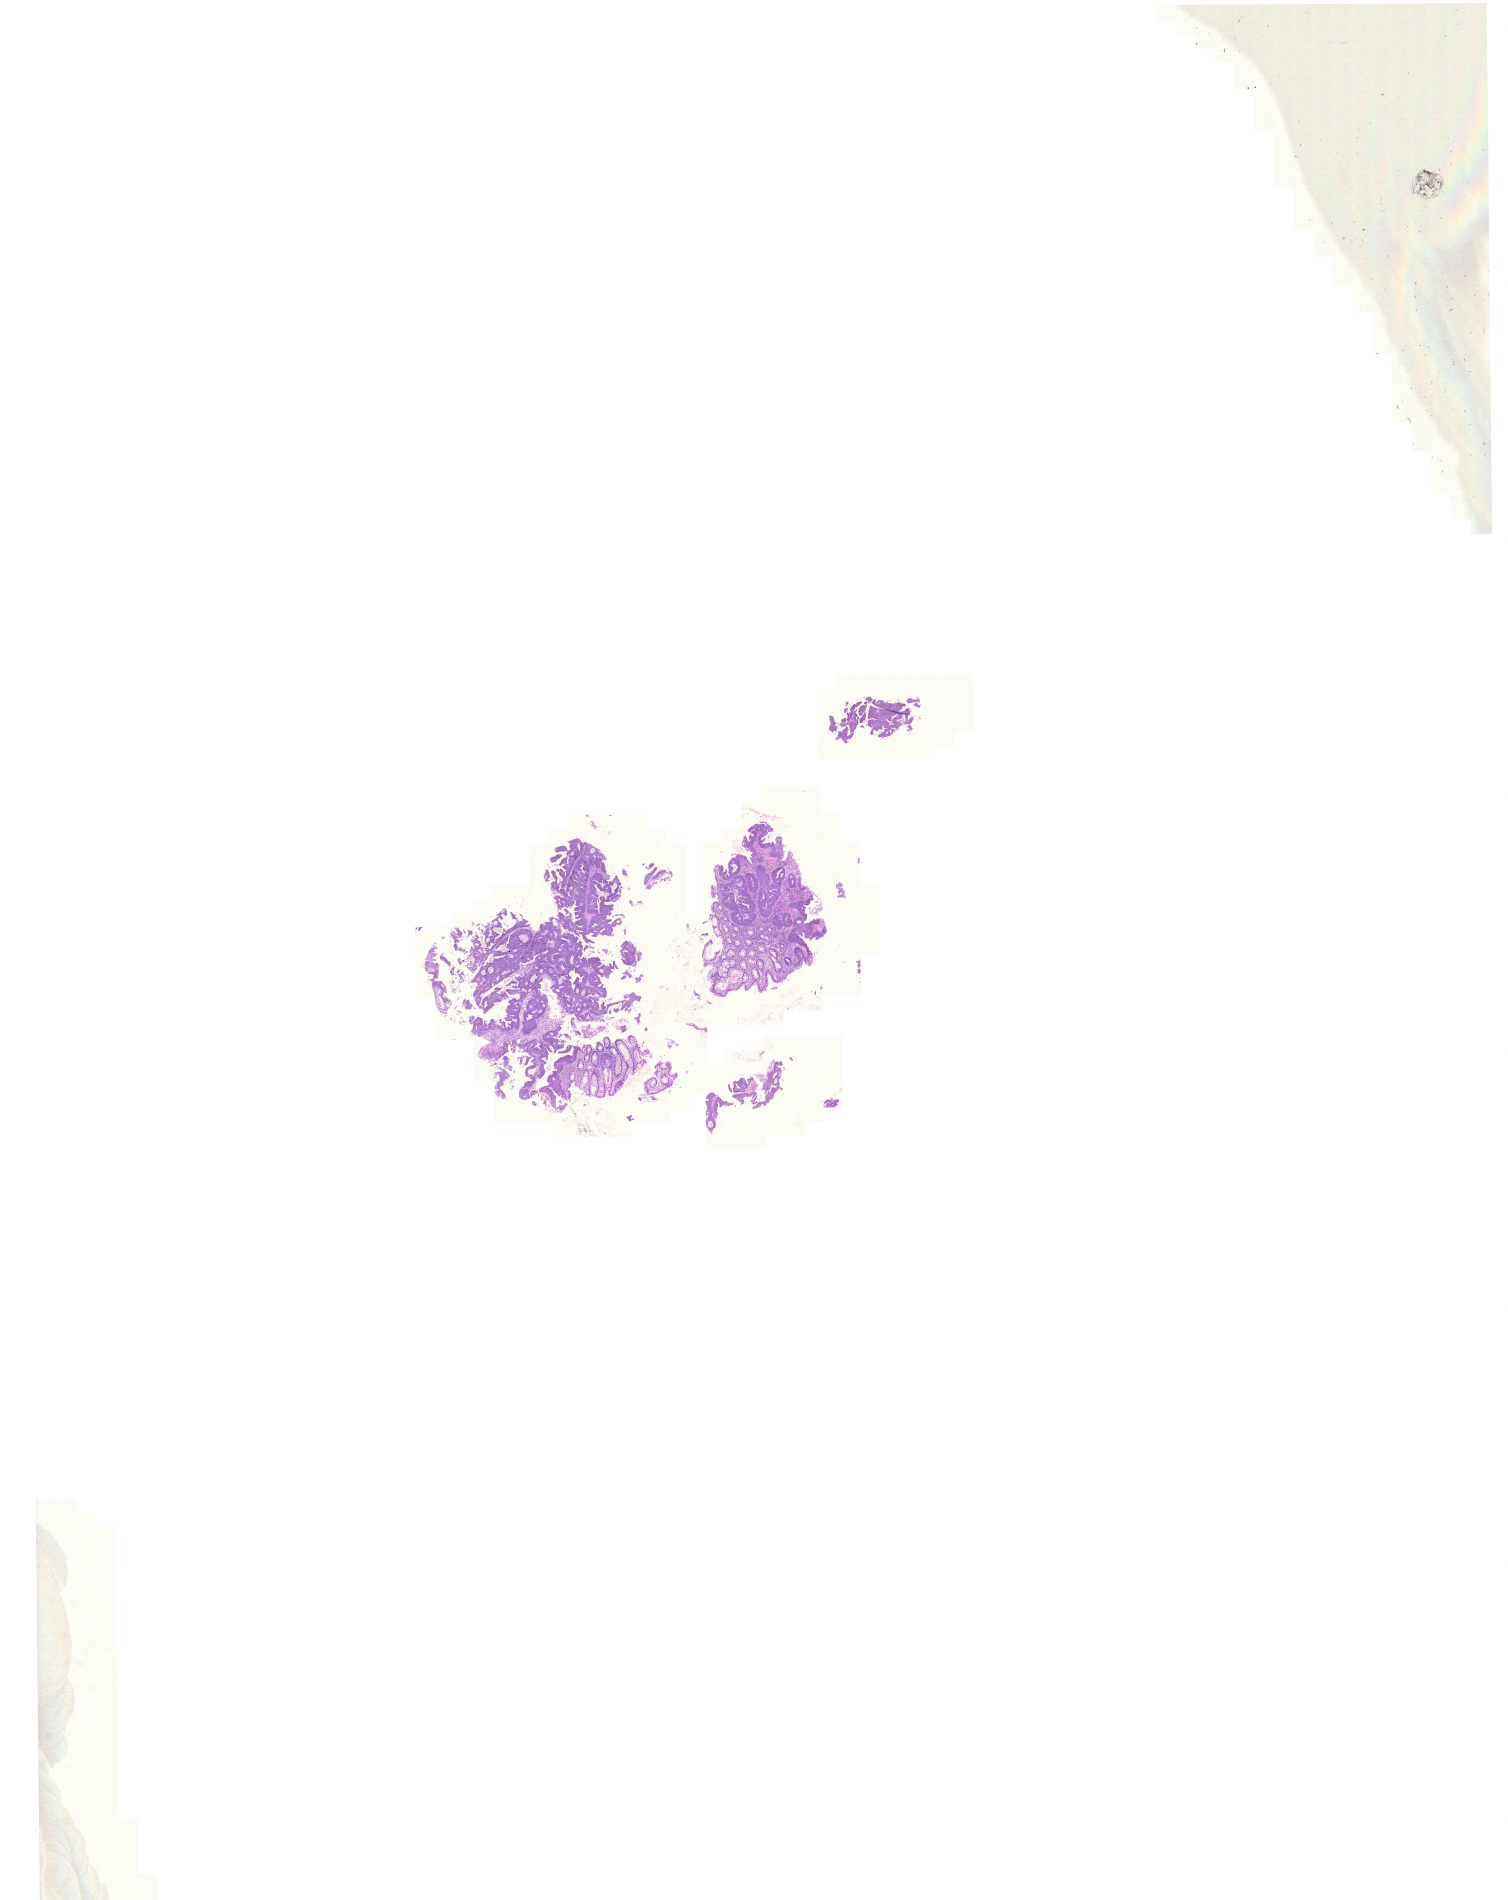
Whole-slide histology image, H&E — a low-resolution overview of the entire scanned area, about 22.4 x 28.3 mm; formalin-fixed paraffin-embedded (FFPE) diagnostic section; rectum, primary tumour sample. Female patient; age at initial diagnosis 62 years.
Diagnosis: Adenocarcinoma, NOS. Lymph nodes positive (case pathology): 0 of 11 examined. AJCC pathologic stage: I (5th edition).